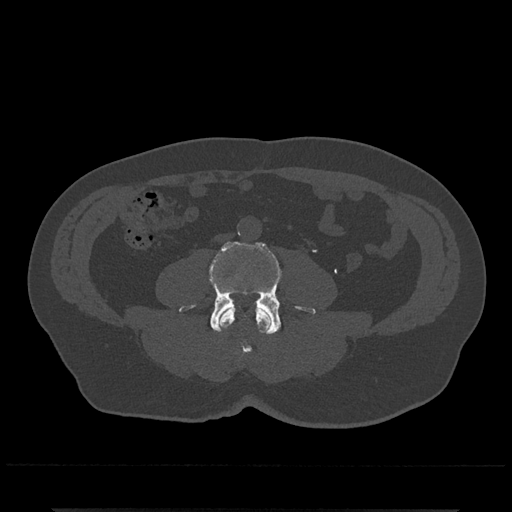
CT including the spine, one axial slice; position 175 of 797 along the scan axis; reconstruction kernel Br40s/3; bone window (W 1800 / L 400 HU); 0.5 mm slice thickness; 512 × 512 image matrix. Male patient, age 67 years. Case-level facts recorded for this patient, not image findings: primary cancer: prostate.
Annotated regions visible in this slice (semi-automatic segmentation, software-assisted and operator-edited):
- L3 vertebra: bounding box <219,307,272,355> (left, top, right, bottom; pixels)
- L4 vertebra: <179,242,316,335>